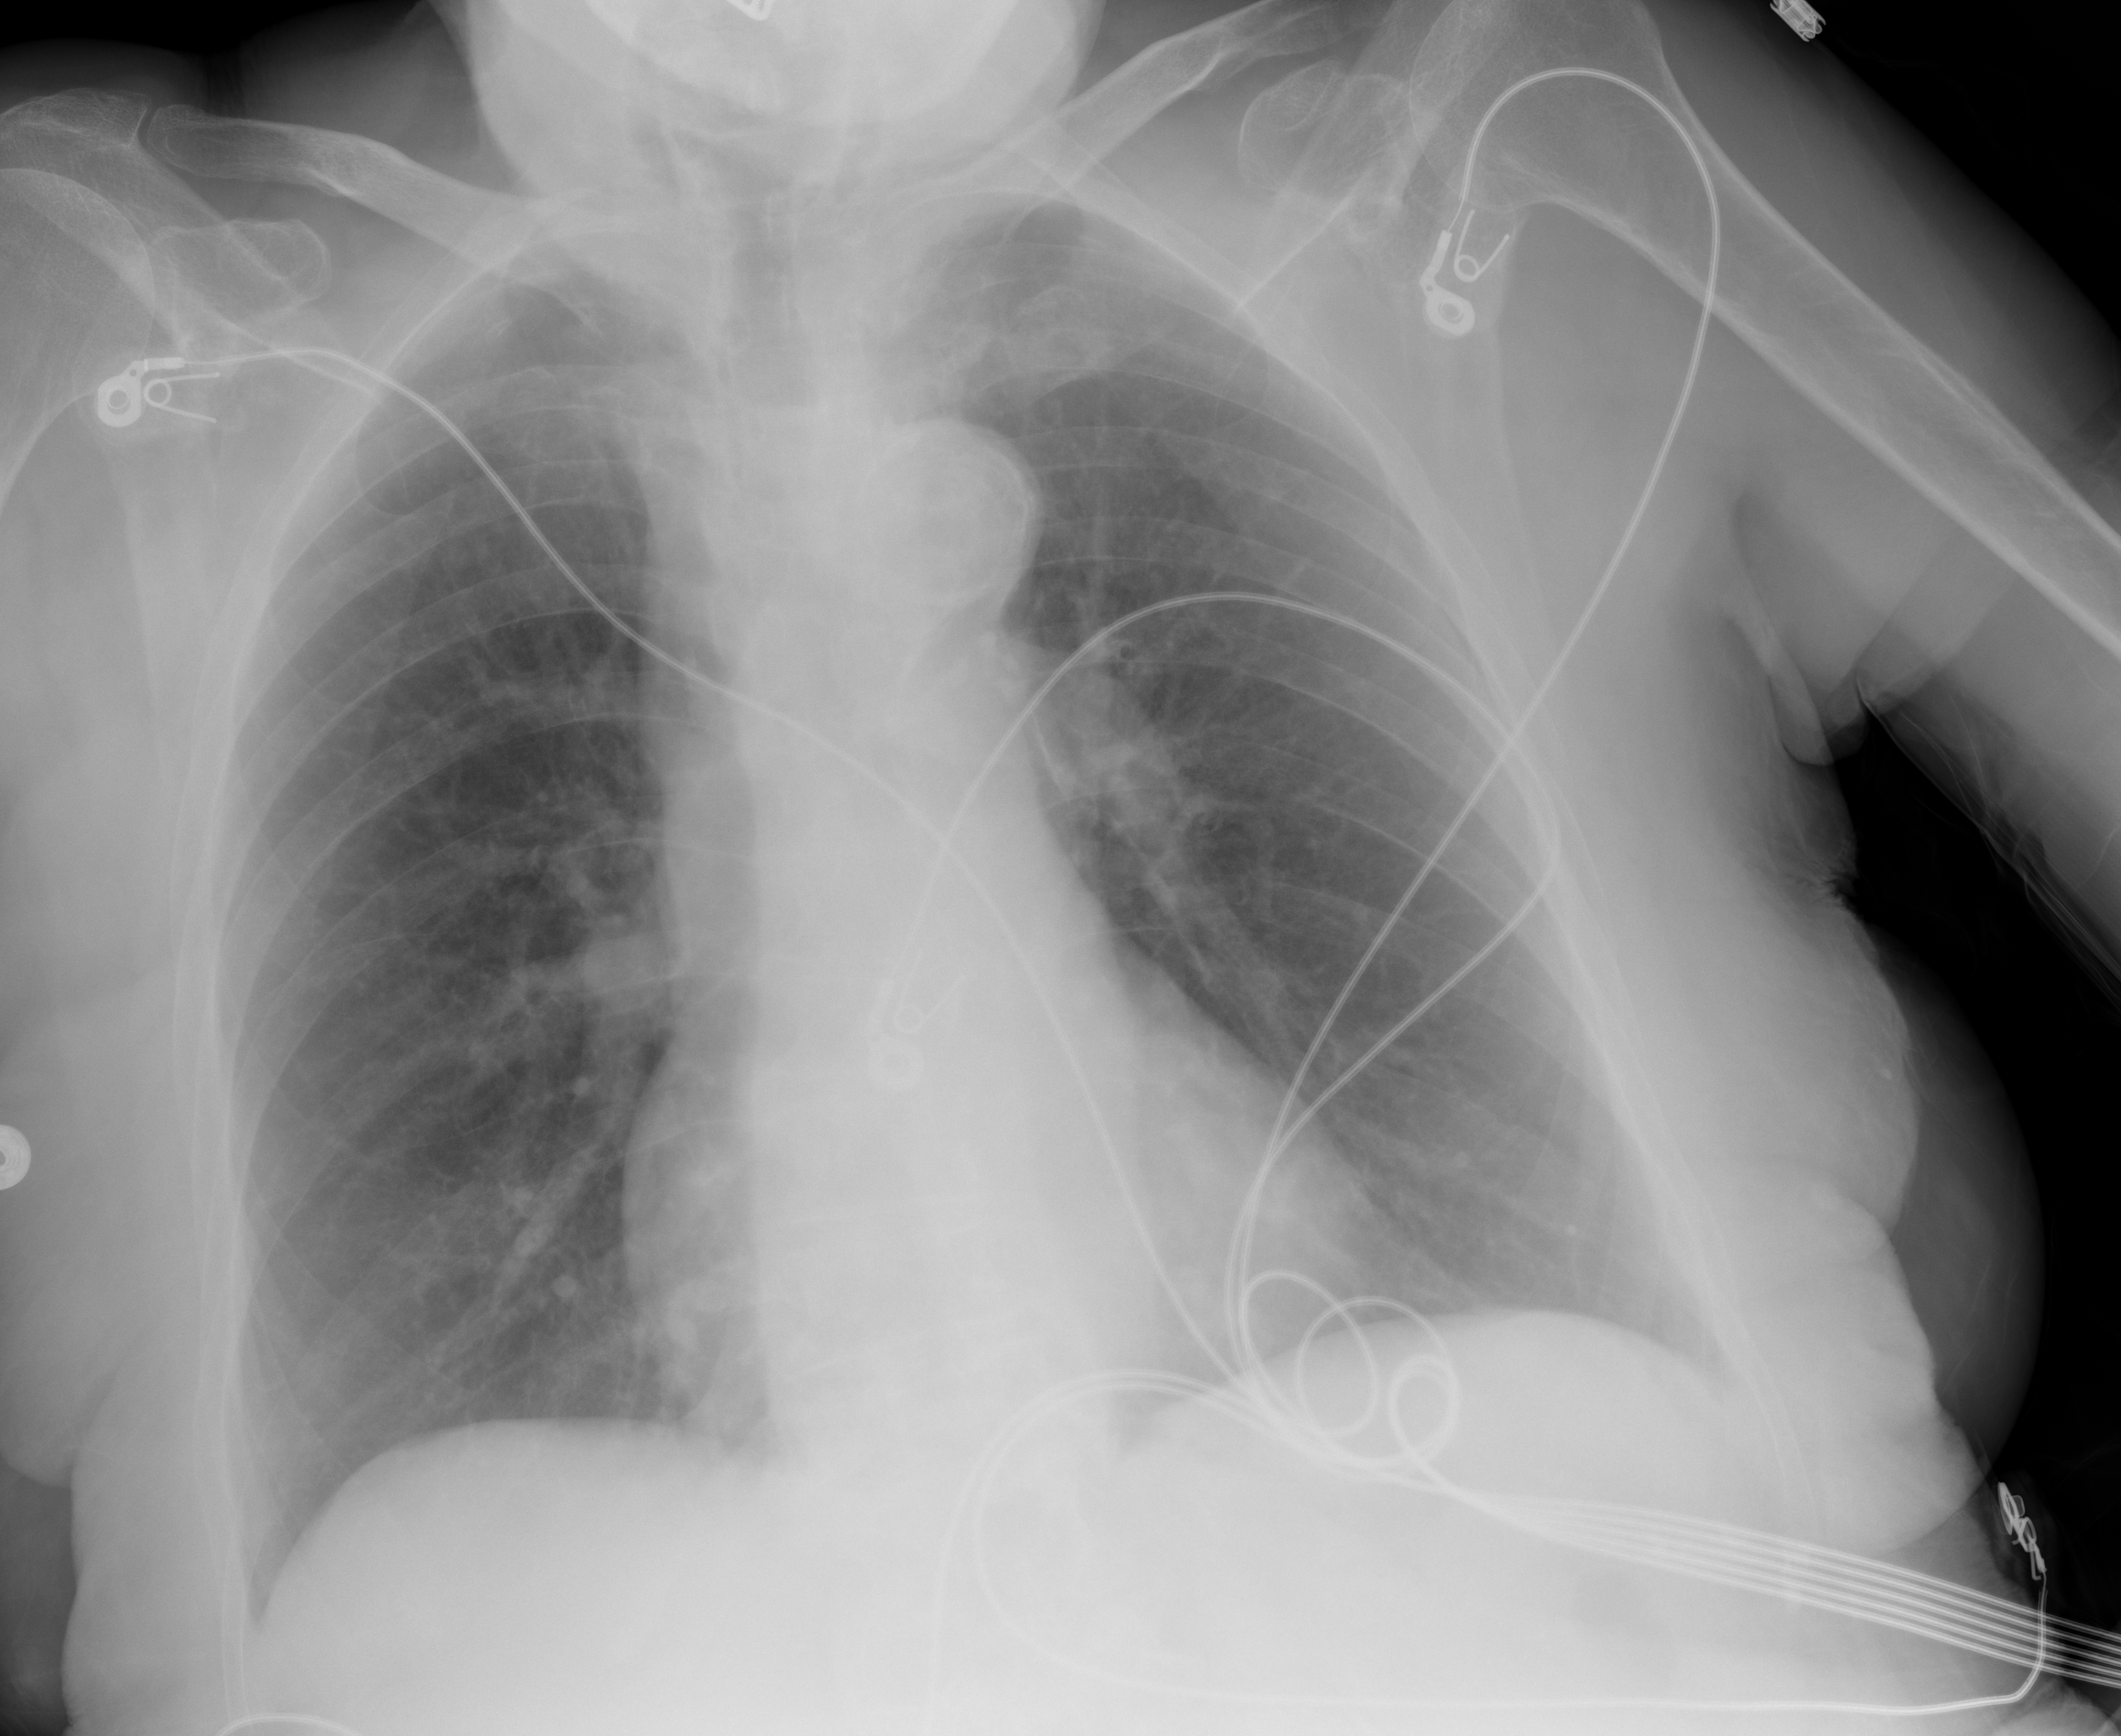
Portable chest radiograph, AP projection. Female patient, aged 90 years or older; imaged 0 days after the COVID-19 diagnosis.
Radiologist's key findings for this exam: The lungs are clear.